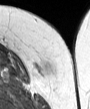
MRI of an extremity soft-tissue mass, one axial slice; position 8 of 45 along the scan axis; MR volume resampled by the dataset authors to the PET/CT grid (not the native acquisition matrix); 90 × 109 image matrix, field of view 88 × 106 mm. Female patient. Case-level facts recorded for this patient, not image findings: histological type: leiomyosarcoma; grade: intermediate; site of the primary tumour: parascapusular.
Structures marked on this image (expert contour drawn on MRI and transferred to this co-registered scan by the dataset authors):
- gross tumour volume including surrounding oedema: bounding box <40,66,48,72> (left, top, right, bottom; pixels)